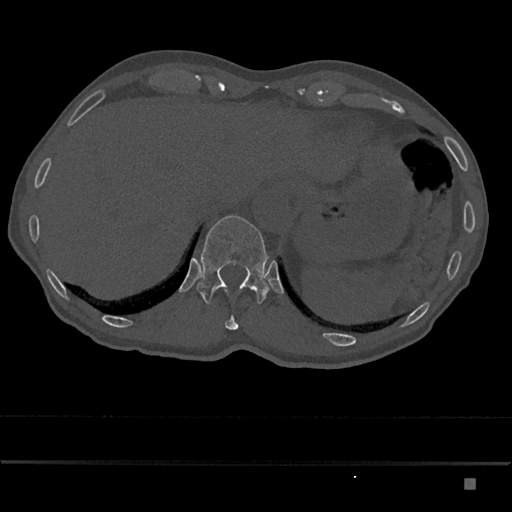
CT including the spine, one axial slice; position 630 of 797 along the scan axis; reconstruction kernel Br40s/3; bone window (W 1800 / L 400 HU); 0.5 mm slice thickness; 512 × 512 image matrix, field of view 390 × 390 mm. Patient: male, 72 years. Case-level facts recorded for this patient, not image findings: primary cancer: prostate.
Outlined on this slice (semi-automatic segmentation, software-assisted and operator-edited):
- T11 vertebra: bounding box <225,316,239,330> (left, top, right, bottom; pixels)
- T12 vertebra: <197,215,269,304>